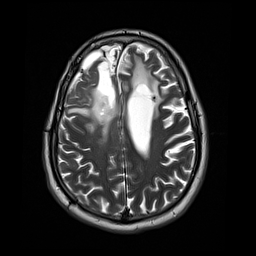
Brain MRI from a brain-tumour surgery series, one axial slice; position 14 of 44 along the scan axis; 4 mm slice thickness; 256 × 256 image matrix, field of view 240 × 240 mm. Case-level facts recorded for this patient, not image findings: histopathology: Astrocytoma; WHO grade: 4; IDH mutation: yes; tumour location: Right Frontal.
Structures marked on this image (outlined manually by an expert reader):
- tumour: bounding box <66,87,114,133> (left, top, right, bottom; pixels)